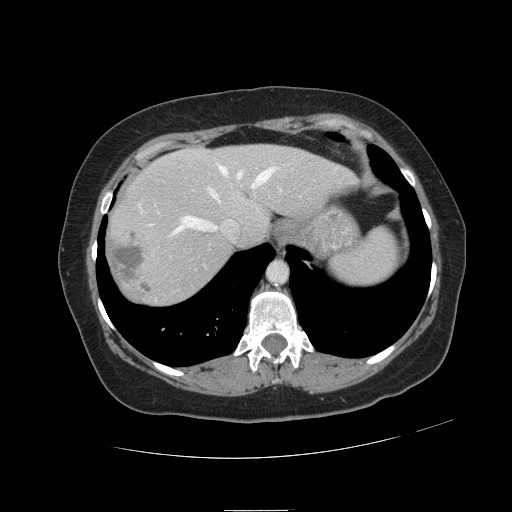
Contrast-enhanced abdominal CT, one axial slice; slice 96 of 121 in the series (ordered by position); intravenous contrast given; soft-tissue window (W 400 / L 40 HU); 2.5 mm slice thickness; 512 × 512 image matrix. Female patient, age 52 years. From the clinical record (not read from this slice): diagnosis: colorectal cancer liver metastases, imaged before liver resection; multiple liver metastases: yes; largest metastasis: 6.3 cm; chemotherapy before resection: yes.
Outlined on this slice (expert manual segmentation):
- hepatic veins: bounding box [x1, y1, x2, y2] px = [139, 165, 275, 234]
- liver: [106, 145, 353, 307]
- planned liver remnant (the part of the liver to remain after resection): [169, 145, 353, 243]
- portal vein (with intrahepatic branches): [279, 189, 281, 191]
- liver metastasis: [111, 245, 143, 282]